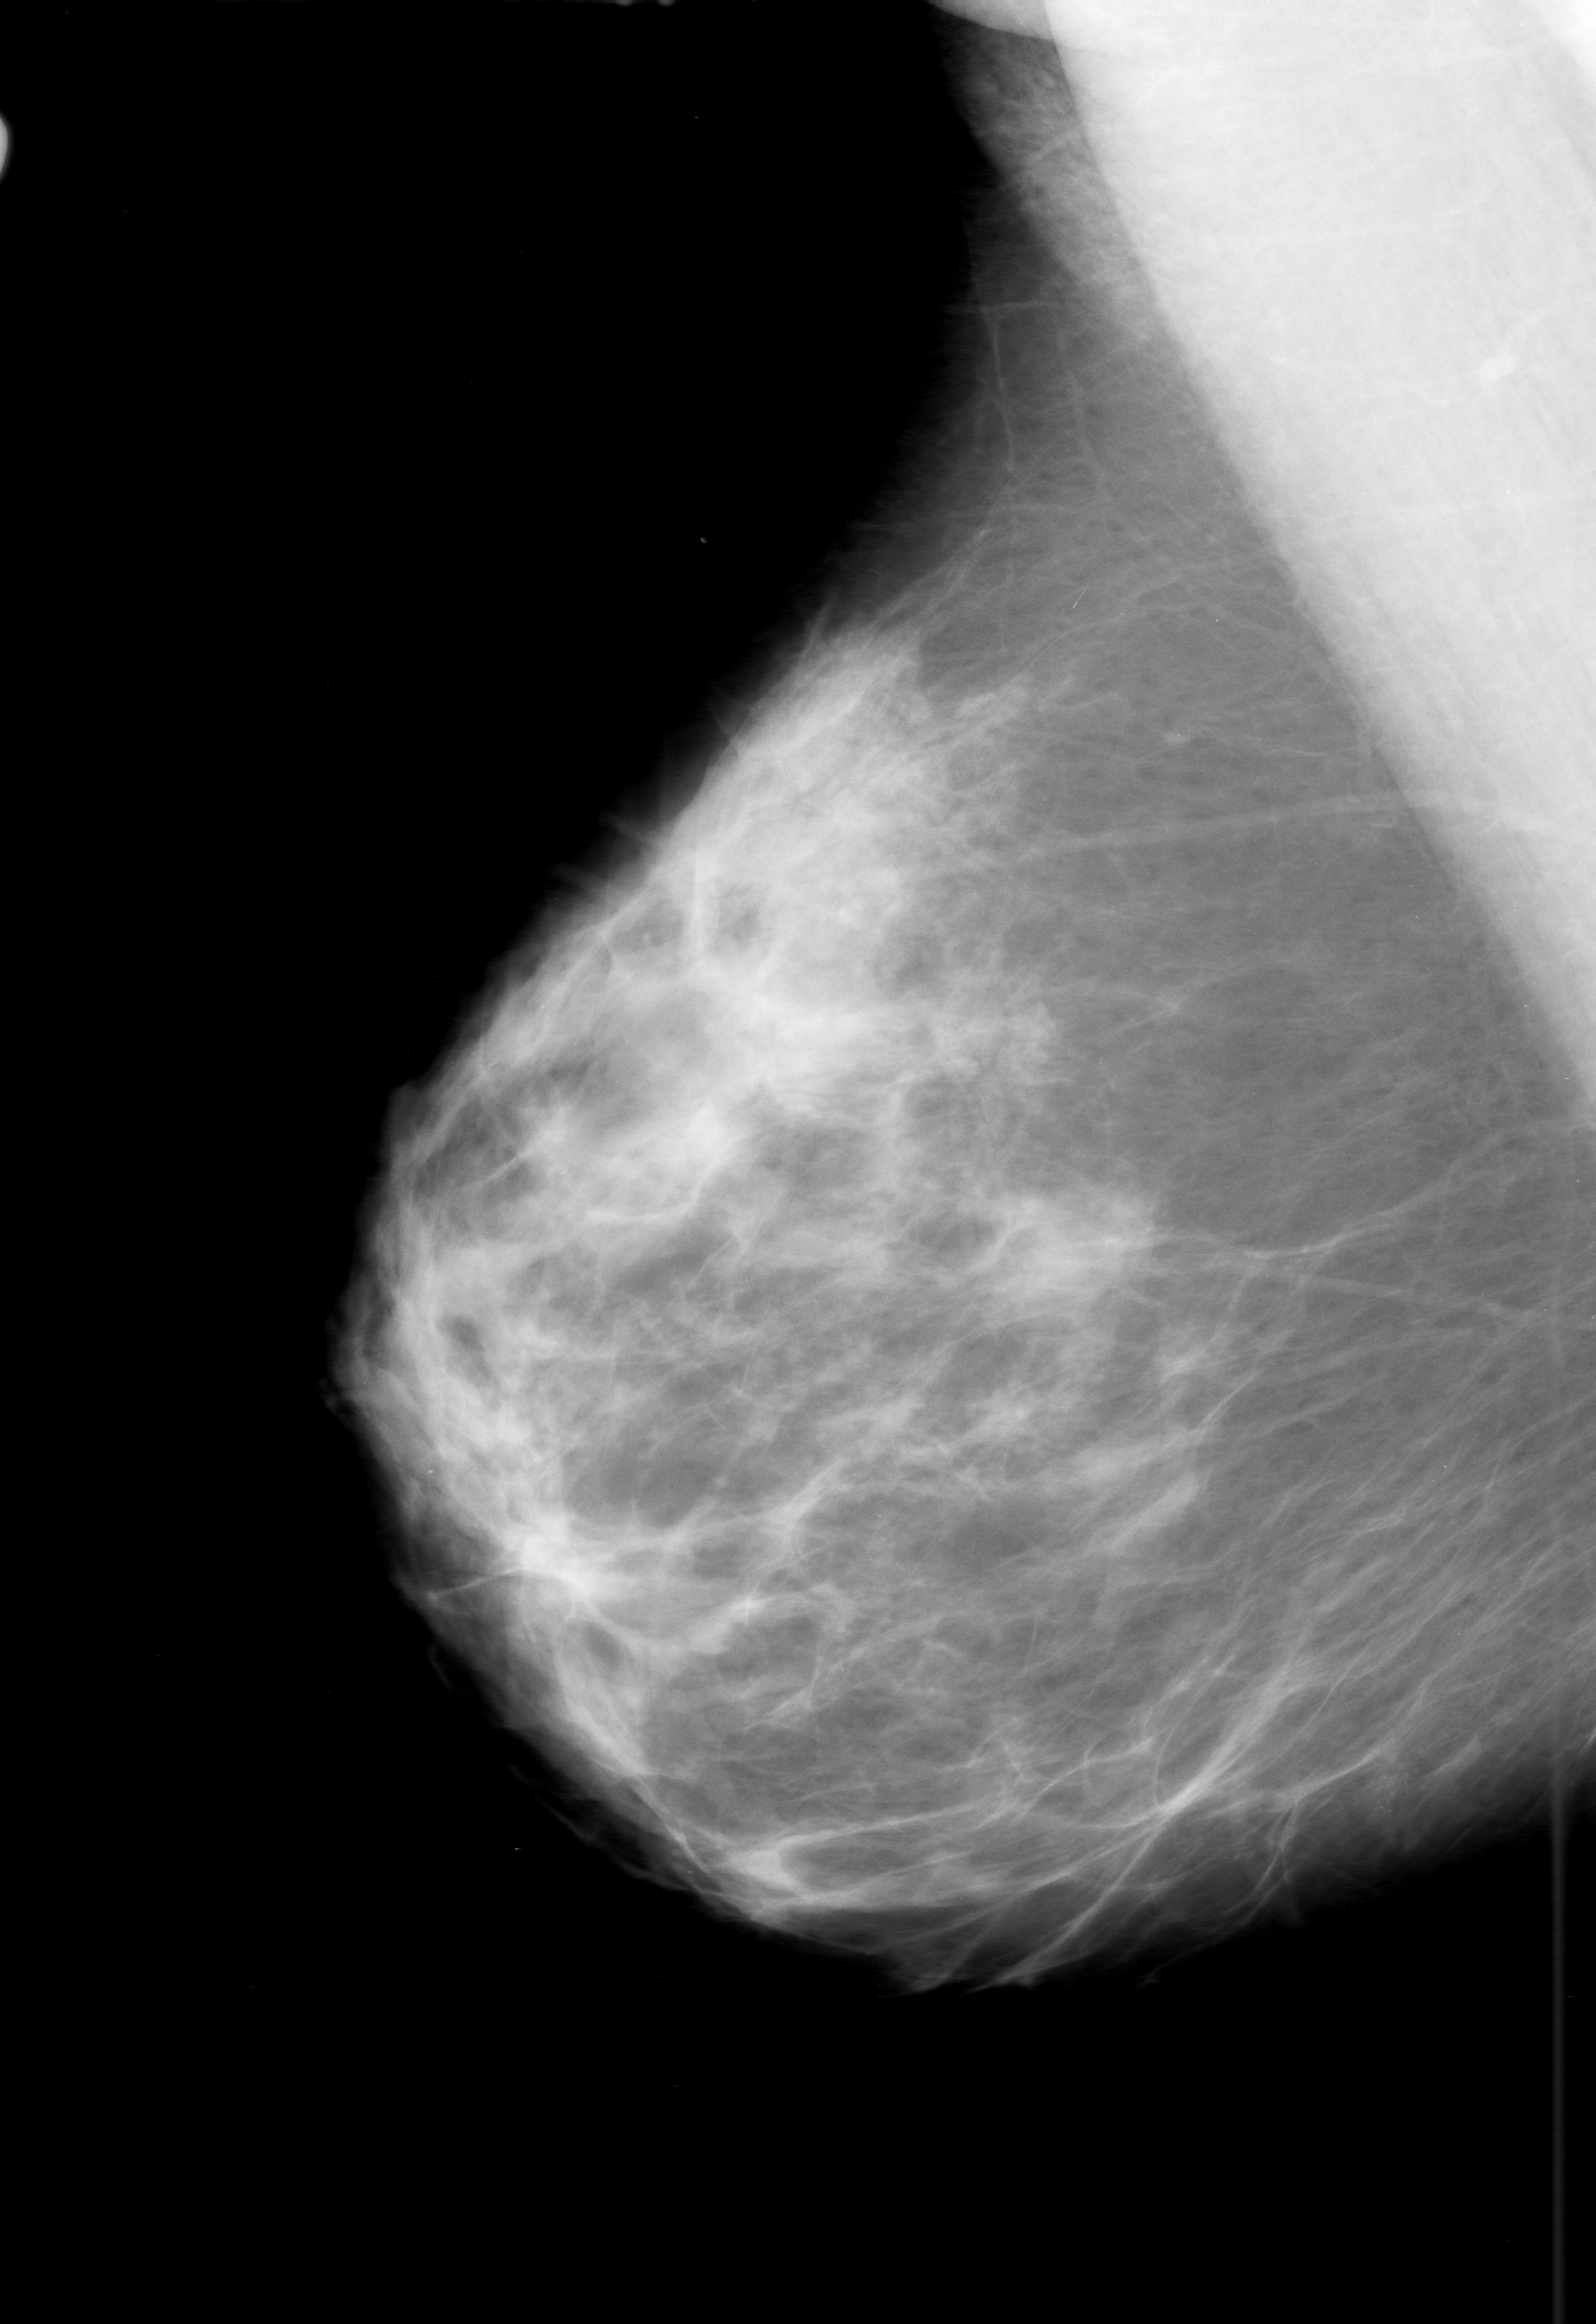
Digitized screen-film mammogram. Right breast. MLO view. Breast composition: scattered fibroglandular densities (BI-RADS density category 2 of 4). 1596 × 2324 image matrix.
Expert-marked regions of interest on this film, with their recorded descriptors:
- calcifications, morphology punctate, distribution clustered; BI-RADS assessment category 0 (incomplete: needs additional imaging); pathology (as recorded): benign: bounding box <1272,1683,1513,1896> (left, top, right, bottom; pixels)